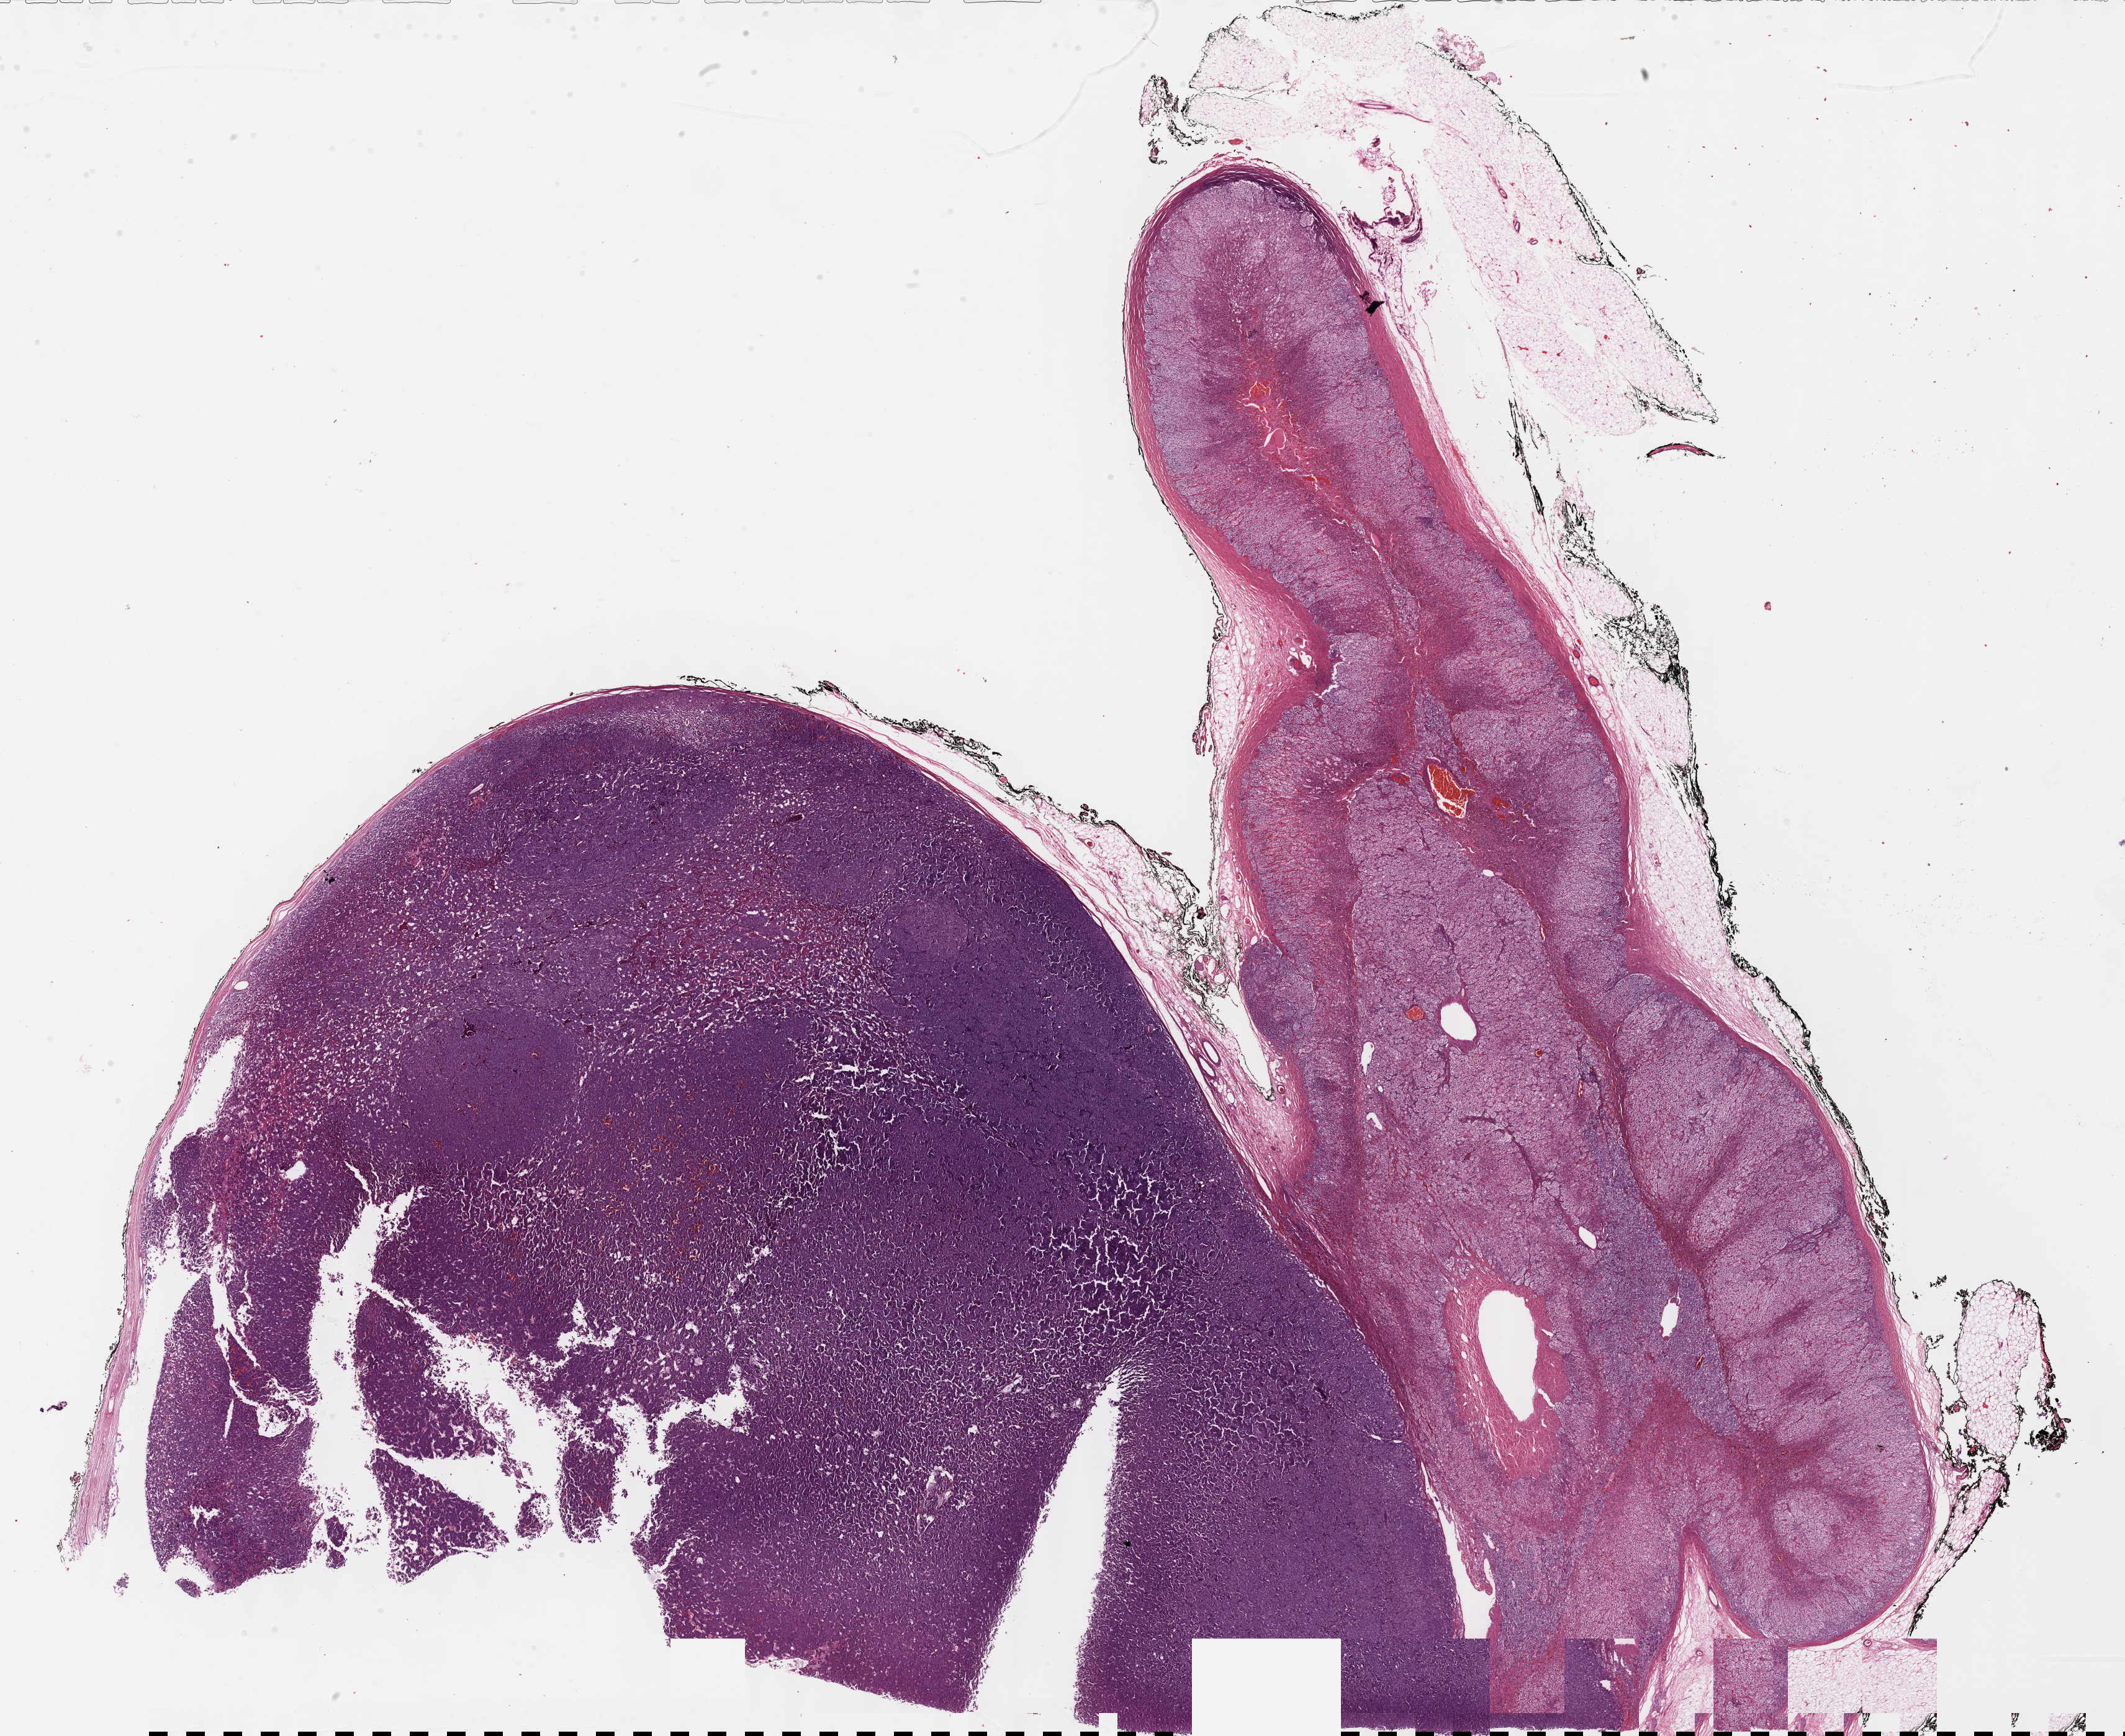
Digitized Hematoxylin and eosin (H&E) stained tissue section (whole slide), low-resolution overview of the scanned area, about 27.7 x 22.6 mm (acquisition: 40x scan); formalin-fixed paraffin-embedded (FFPE) diagnostic section; primary tumour sample from the adrenal gland. Female patient; age at initial diagnosis 45 years.
Diagnosis: Pheochromocytoma, NOS.